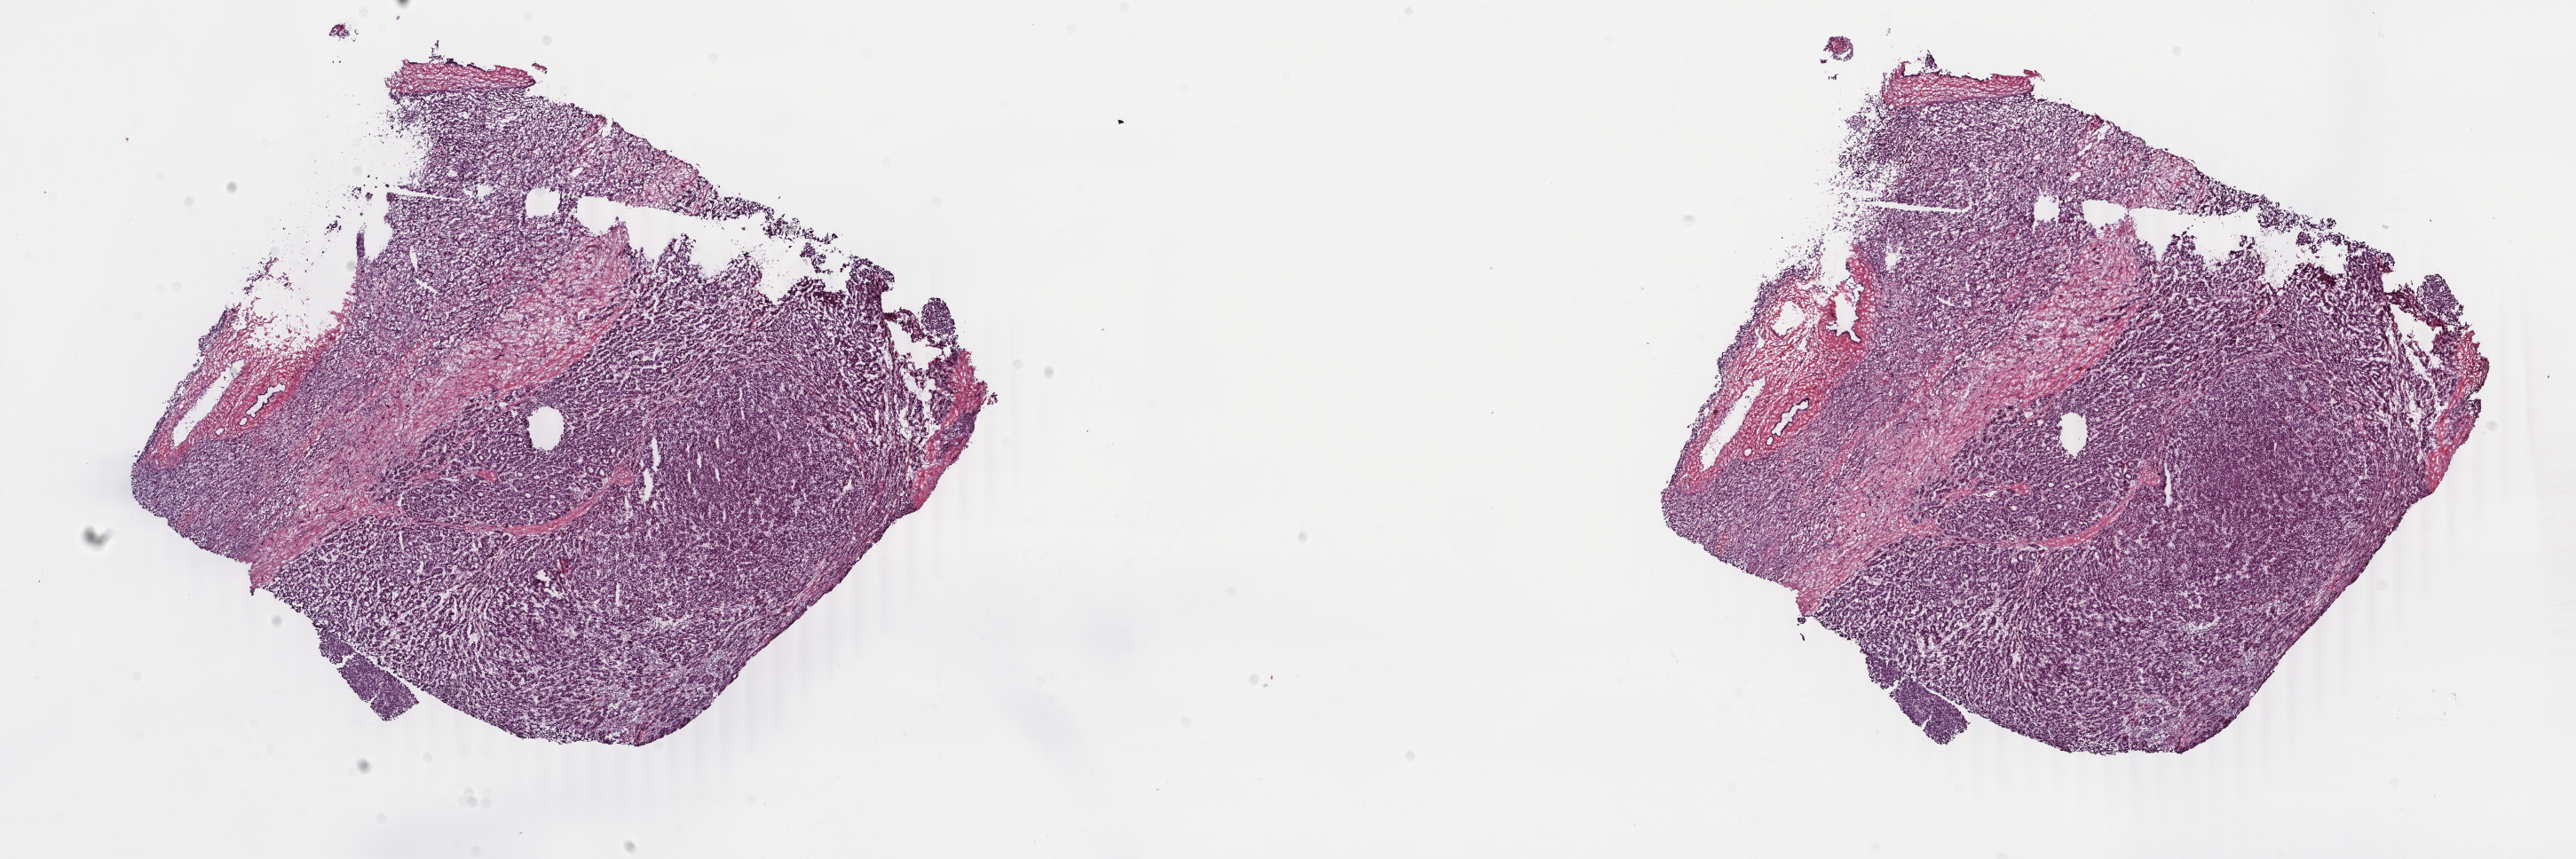
Digitized H&E tissue section (whole slide) — whole scanned area (about 23.1 x 7.7 mm, from a 40x scan) shown as a low-resolution overview; frozen section; liver, primary tumour sample. Patient: female, age at initial diagnosis 61 years. Histologic grade: G2 (moderately differentiated). Slide review estimates, as recorded: tumour cells 85%, tumour nuclei 75%, normal cells 5%, stromal cells 10%, necrosis 0%. Inflammatory infiltration, as recorded: lymphocyte infiltration 2%, monocyte infiltration 0%, neutrophil infiltration 0%.
AJCC pathologic stage: I (6th edition). Pathologic diagnosis: Hepatocellular carcinoma, NOS.